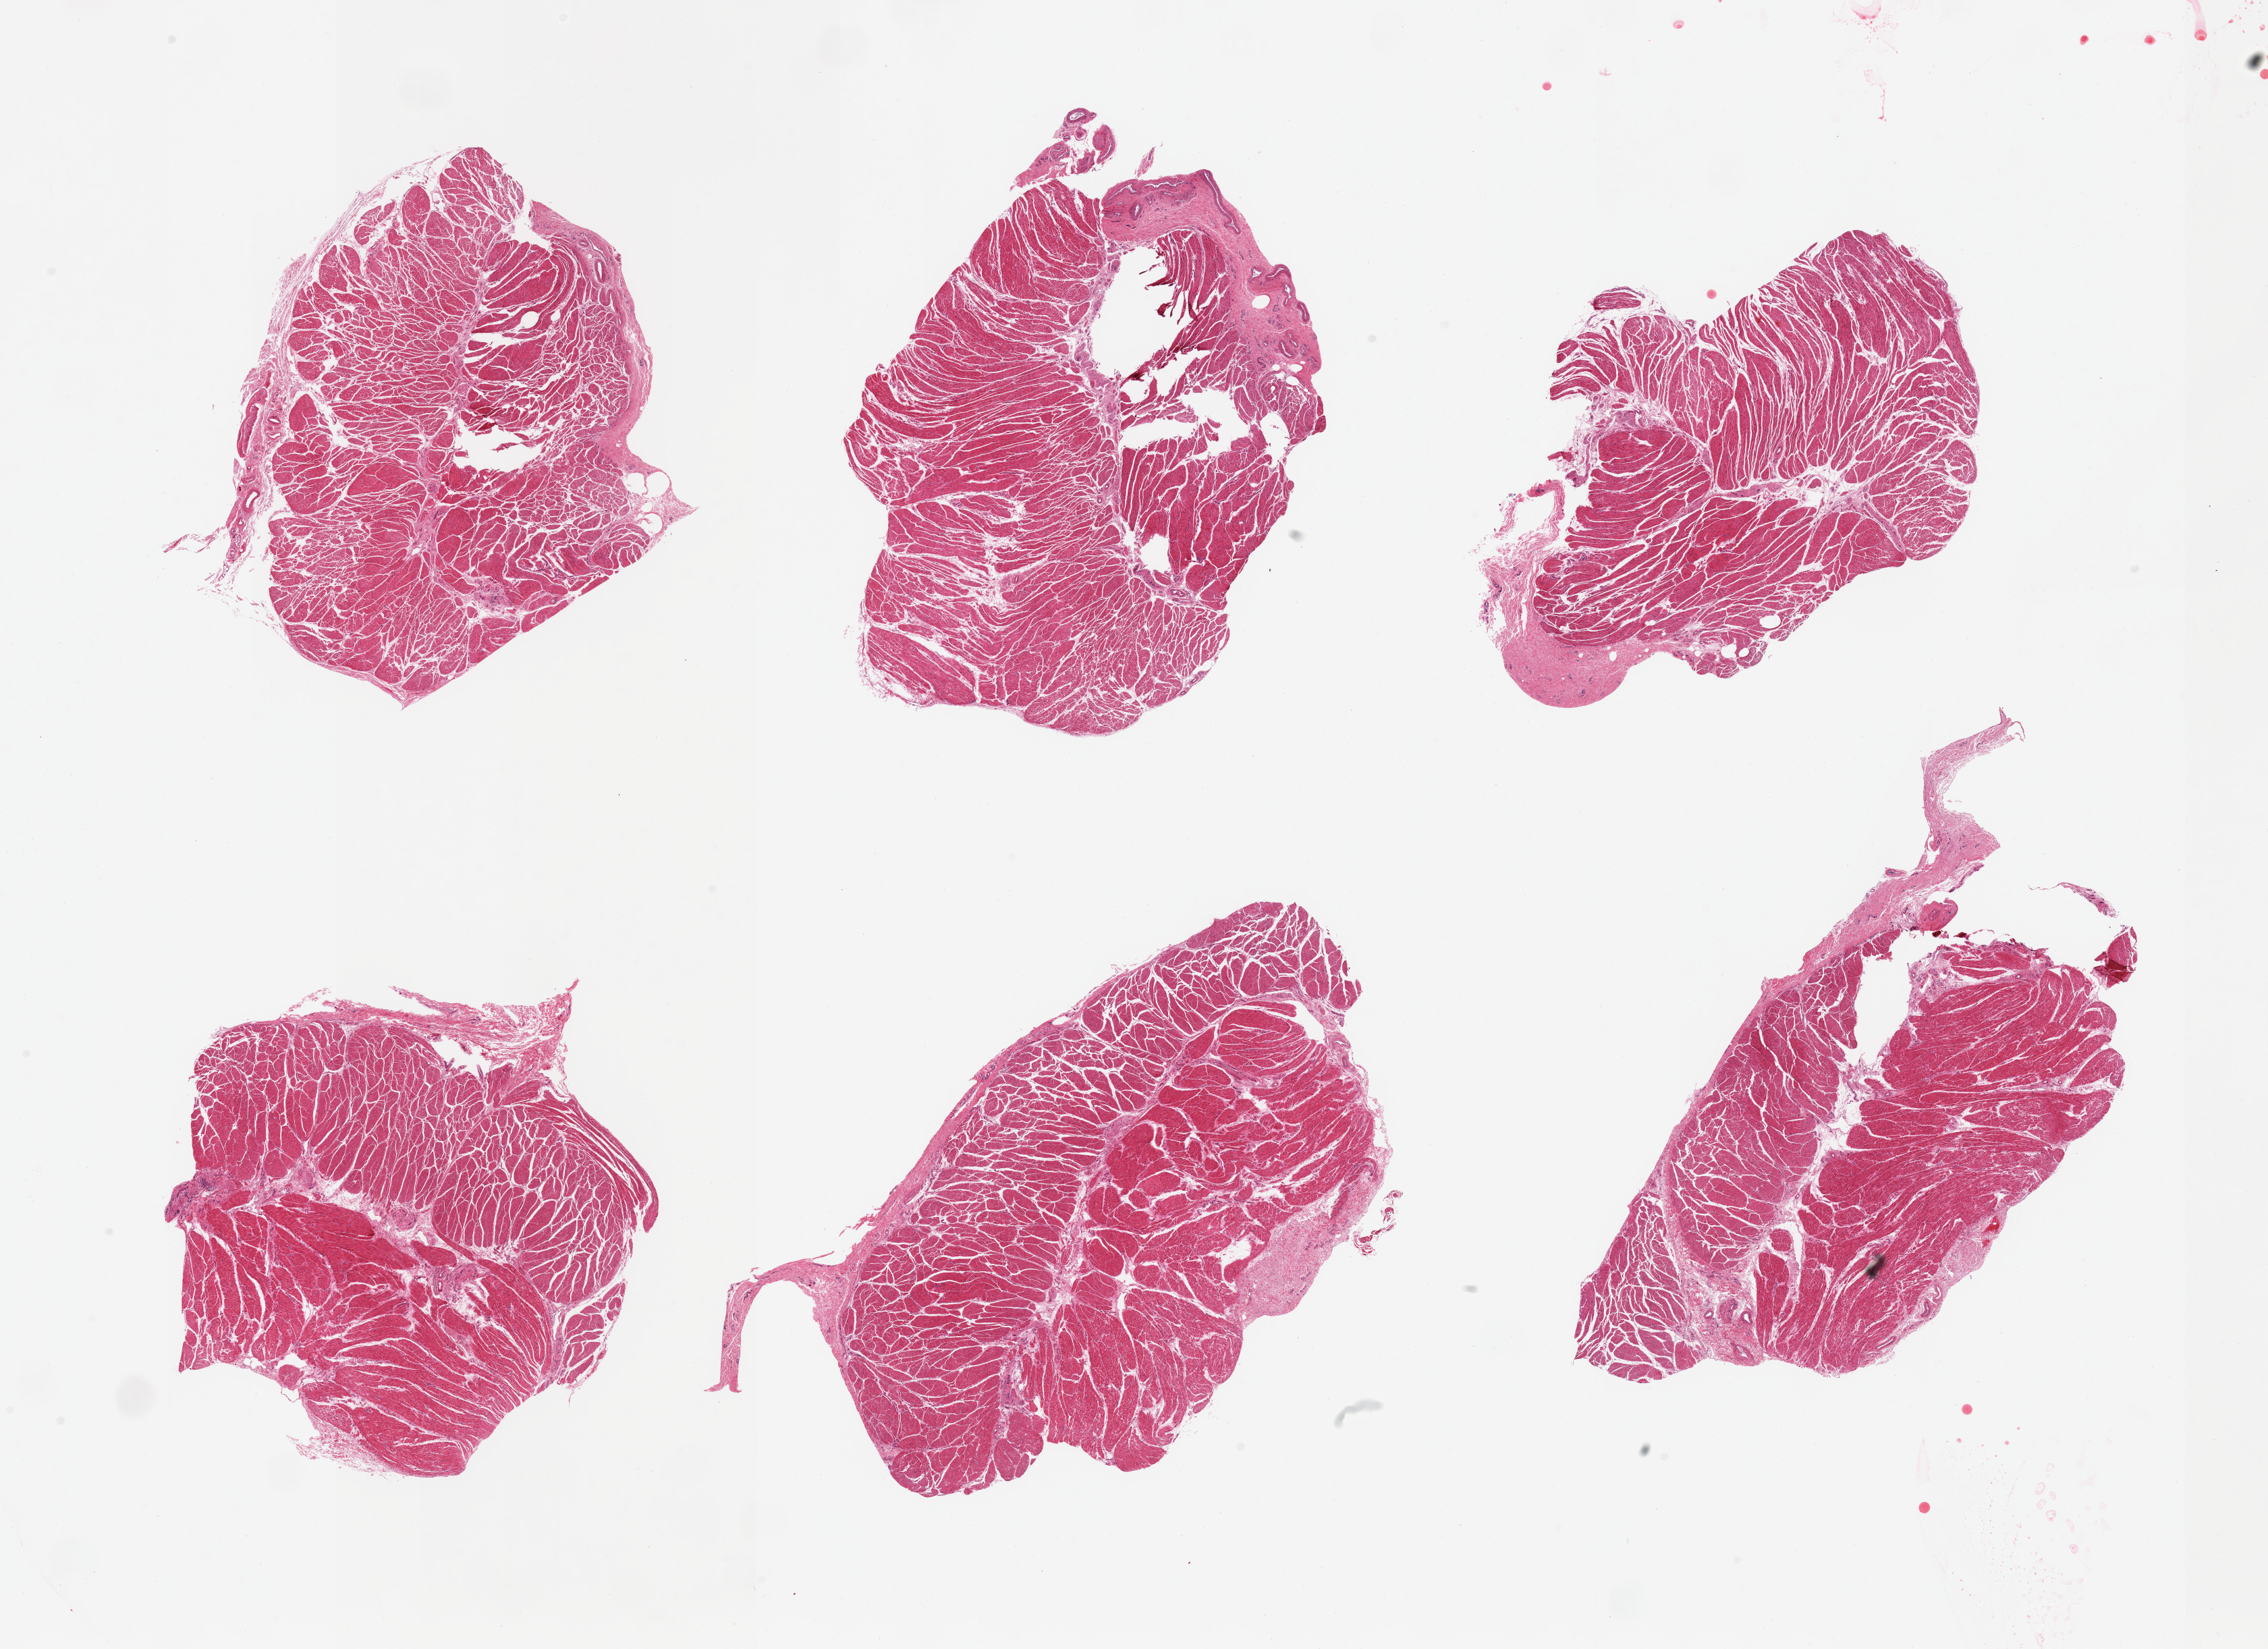
Digitized haematoxylin and eosin-stained section, whole scanned area (about 26.6 x 19.3 mm, acquisition: 20x scan) shown as a low-resolution overview. PAXgene-fixed, paraffin-embedded tissue. Sampled site (target tissue): esophageal mucous membrane. Donor tissue sample. Donor: male.
• reviewer comment on this tissue sample: 6 pieces; target mucosa not present; well trimmed muscularis